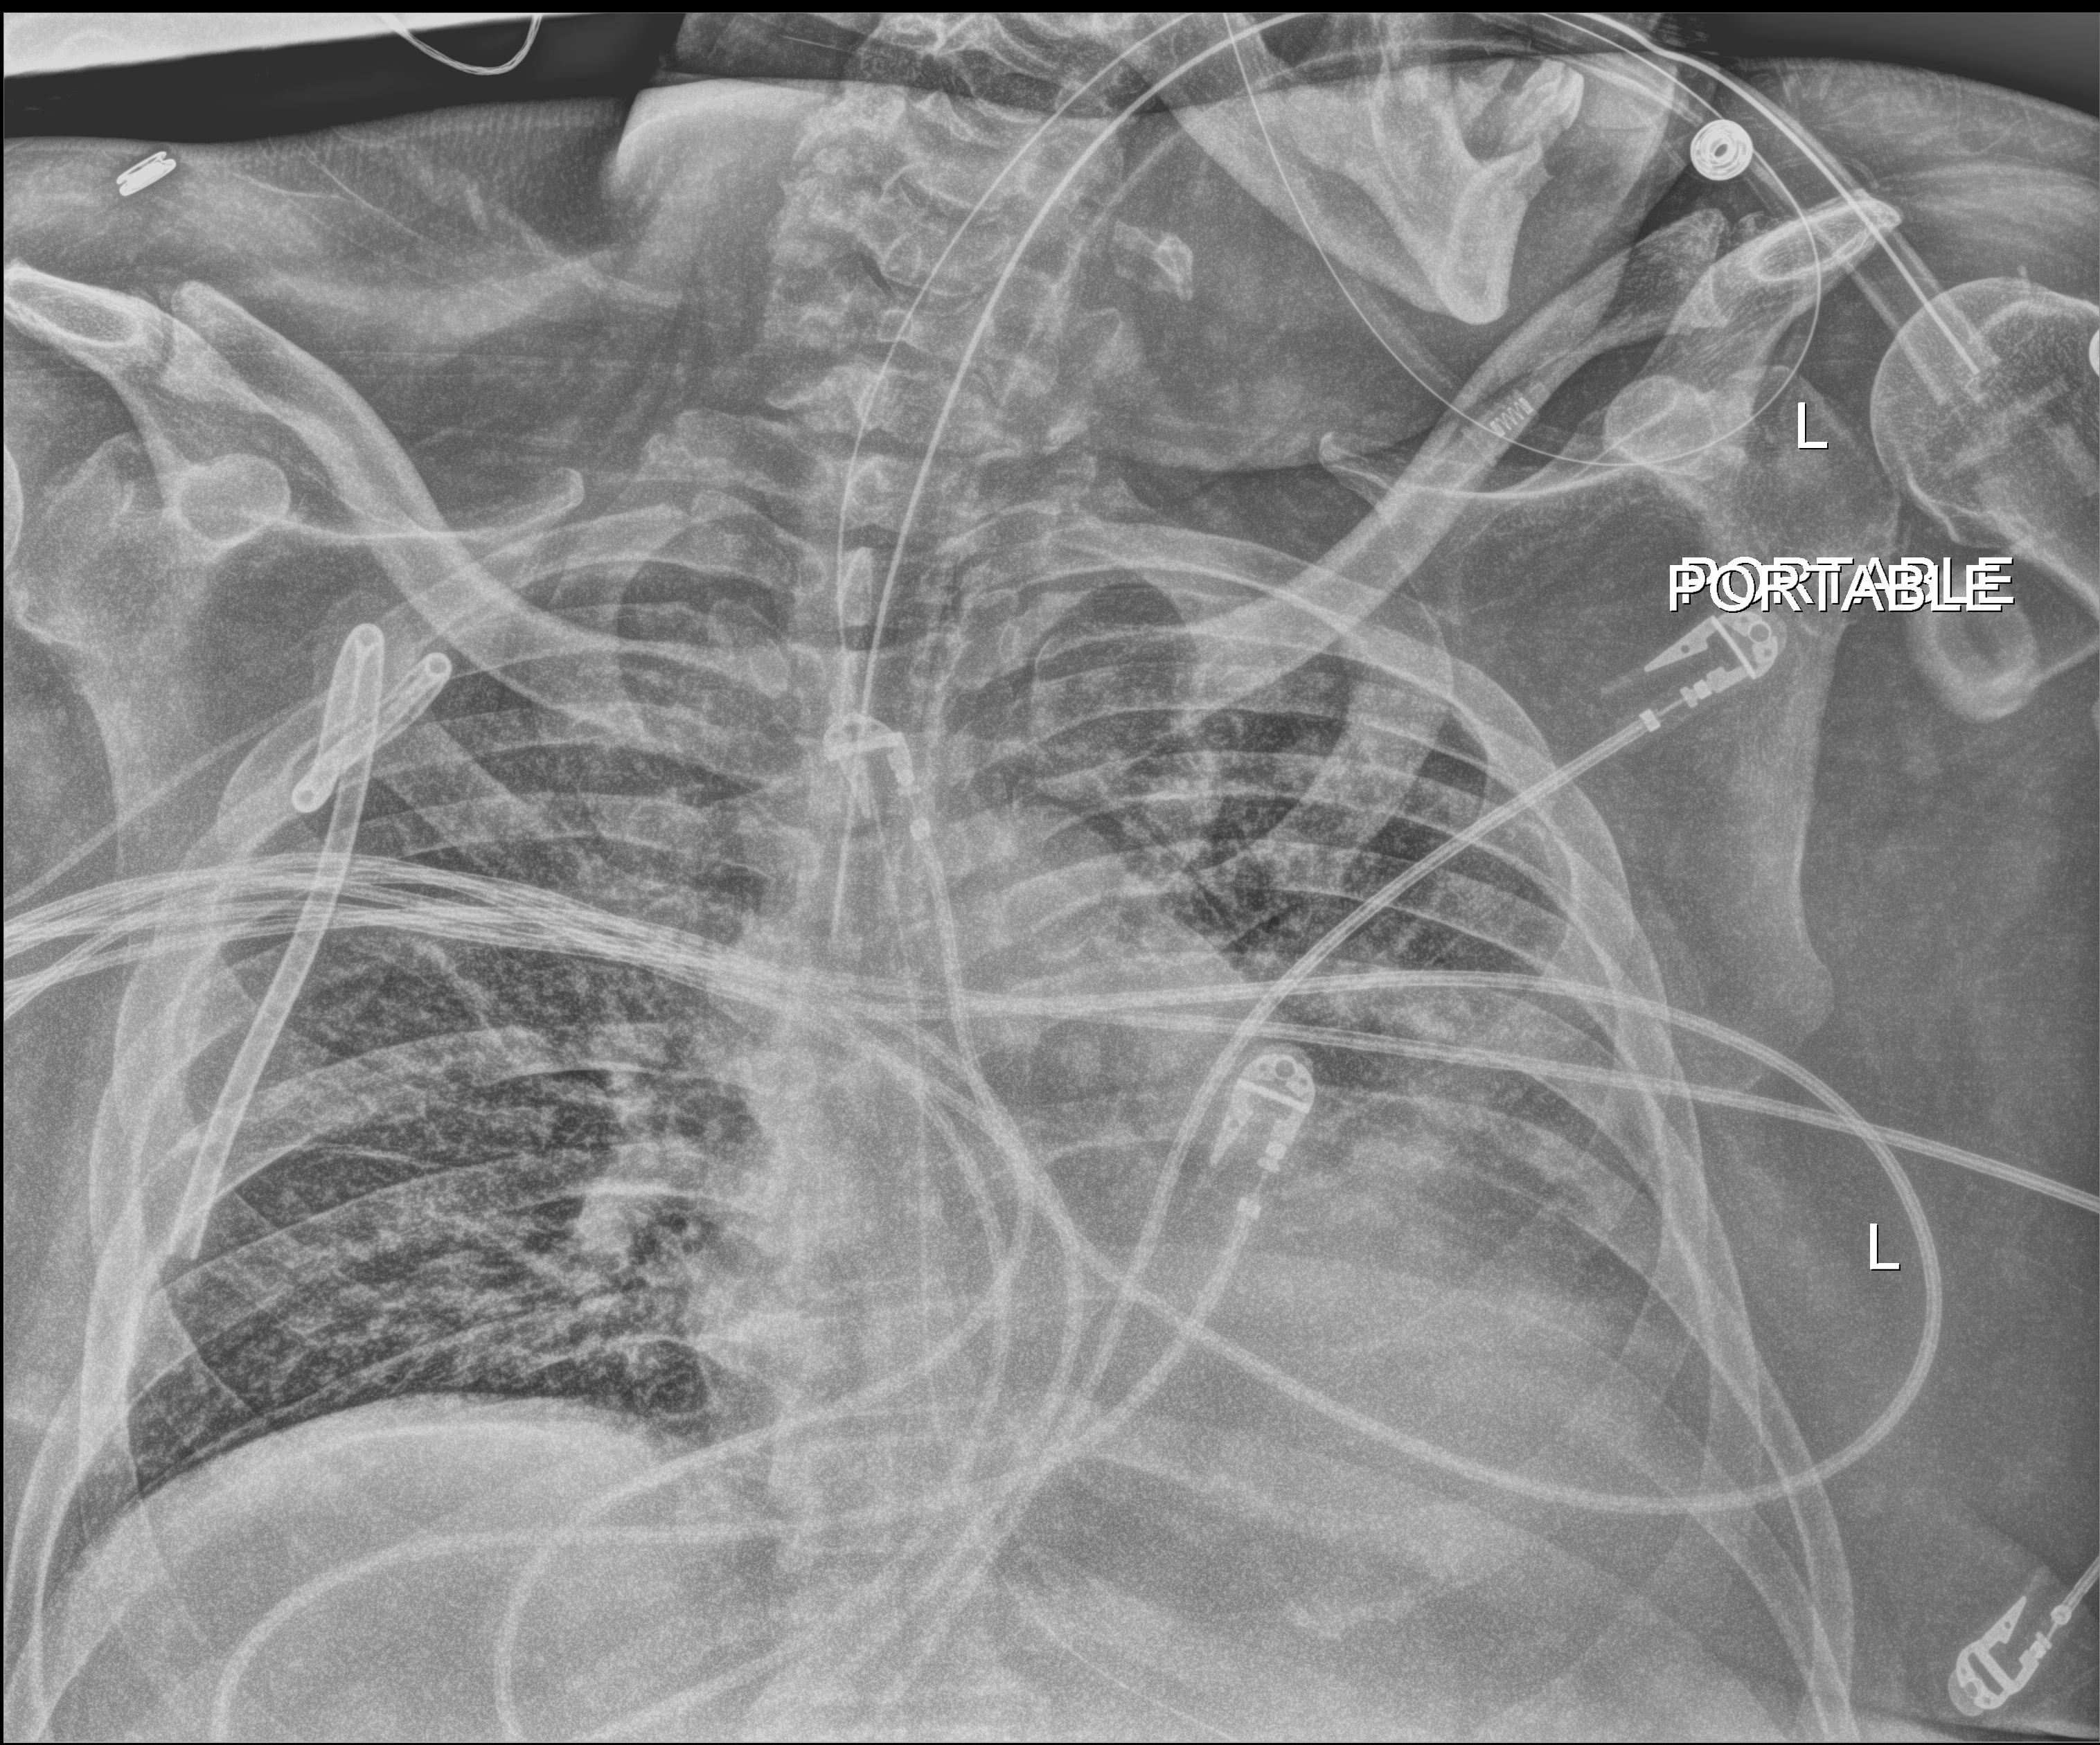
Chest radiograph (digital radiography); anteroposterior (AP) projection. Male patient hospitalised with COVID-19, age 60–74 years.
Hospital-stay facts (about this admission, not read from this image; timing relative to this image not recorded):
- admitted to intensive care during this hospital stay: yes